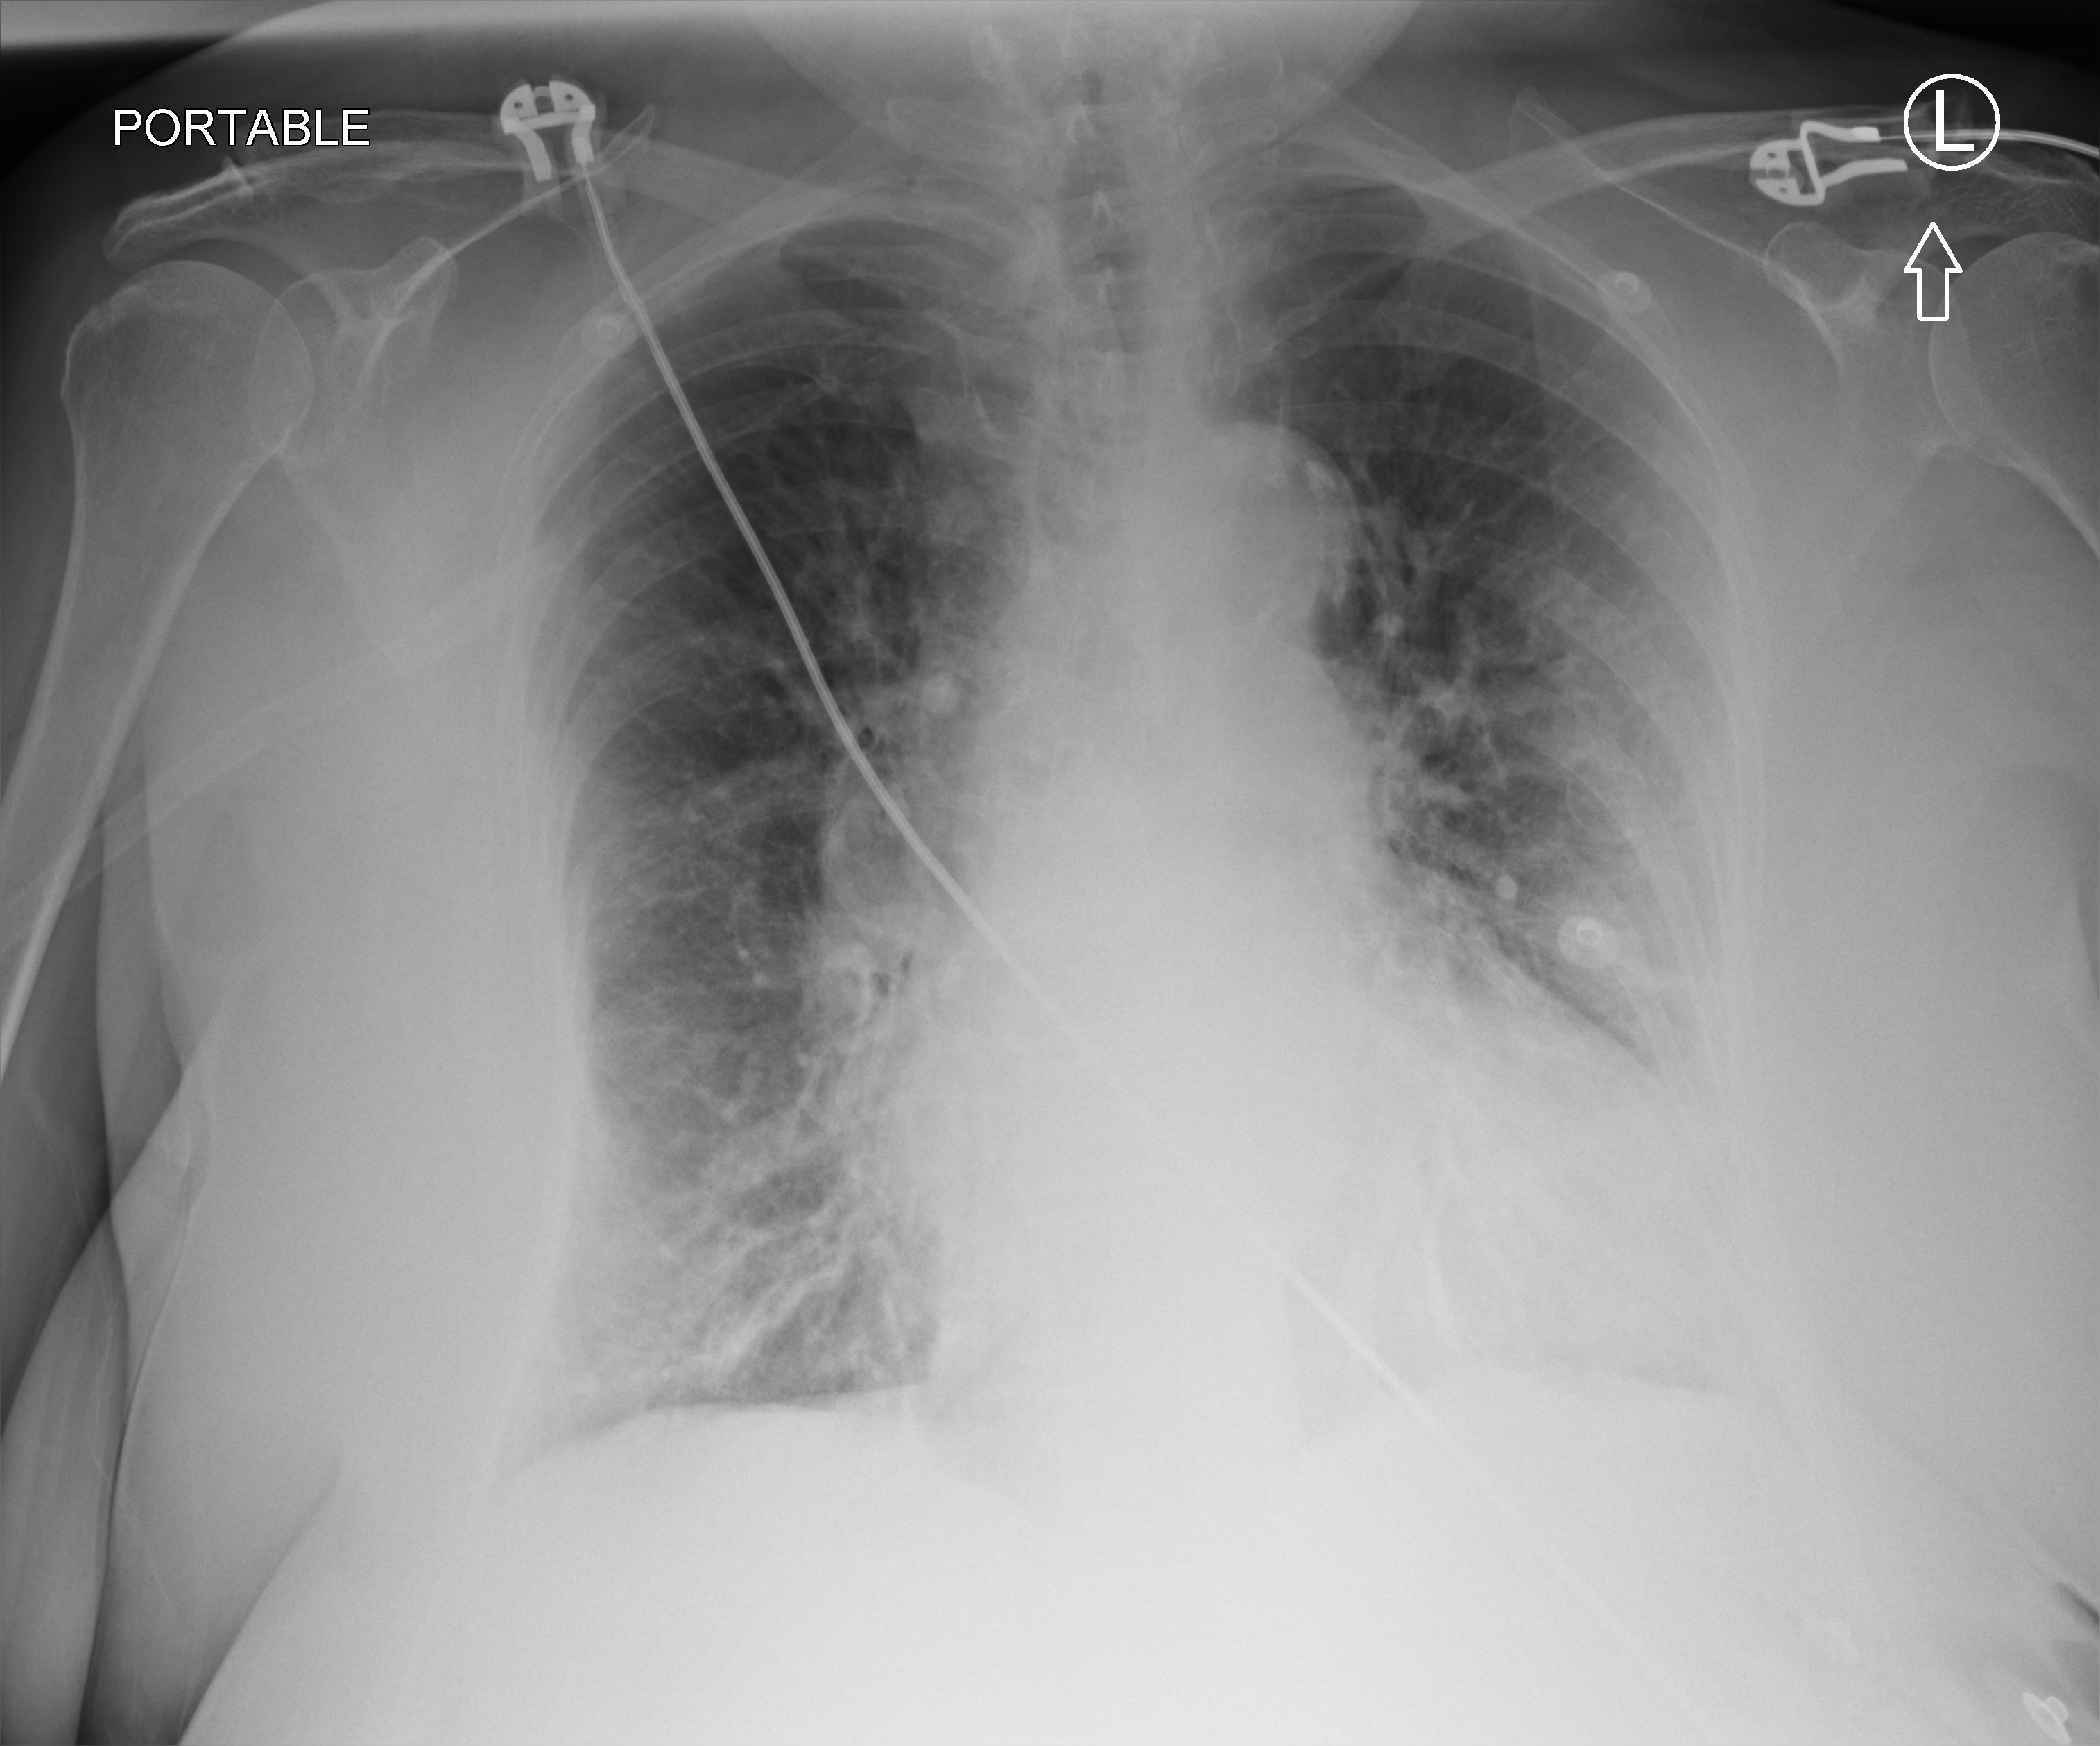
Chest X-ray (portable); anteroposterior (AP) projection. Female patient hospitalised with COVID-19, age 75–90 years.
Hospital-stay facts (about this admission, not read from this image; timing relative to this image not recorded):
- length of hospital stay: 5 days
- mechanically ventilated during this hospital stay: no